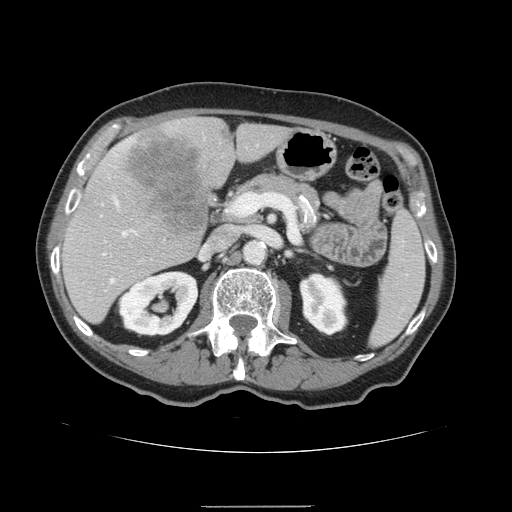
Contrast-enhanced abdominal CT, one axial slice; slice 79 of 168 in the series (ordered by position); 120 kVp; intravenous contrast given; soft-tissue window (W 400 / L 40 HU); 512 × 512 image matrix. Male patient, age 74 years. From the clinical record (not read from this slice): diagnosis: colorectal cancer liver metastases, imaged before liver resection; multiple liver metastases: no; largest metastasis: 14.5 cm.
Annotated regions visible in this slice (manually delineated by an expert):
- hepatic veins: box from (x=112, y=197) to (x=135, y=282) px
- liver: (x=62, y=117)–(x=292, y=325)
- planned liver remnant (the part of the liver to remain after resection): (x=62, y=124)–(x=292, y=325)
- portal vein (with intrahepatic branches): (x=102, y=200)–(x=240, y=261)
- liver metastasis: (x=123, y=128)–(x=210, y=236)